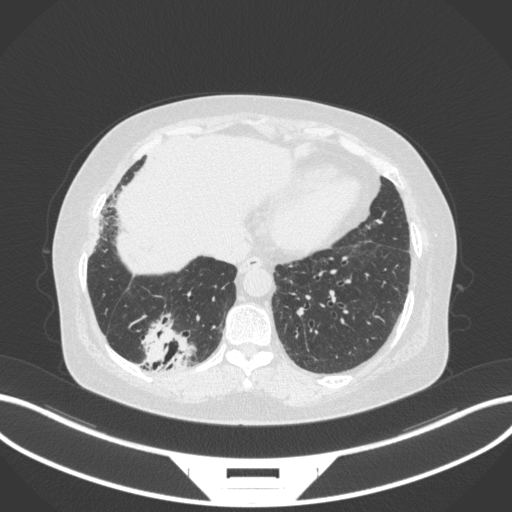
Chest CT, one axial slice. Position 47 of 303 along the scan axis. Reconstruction kernel B31f. 120 kVp. Lung window (W 1500 / L -600 HU). 512 × 512 image matrix, field of view 400 × 400 mm. Patient: female, 65 years. Case-level facts recorded for this patient, not image findings: clinical TNM (as recorded): T2b N1 M0.
Outlined on this slice (rectangle marked by the reading radiologist):
- lung tumour (recorded histology: adenocarcinoma): bounding box <134,313,199,373> (left, top, right, bottom; pixels)